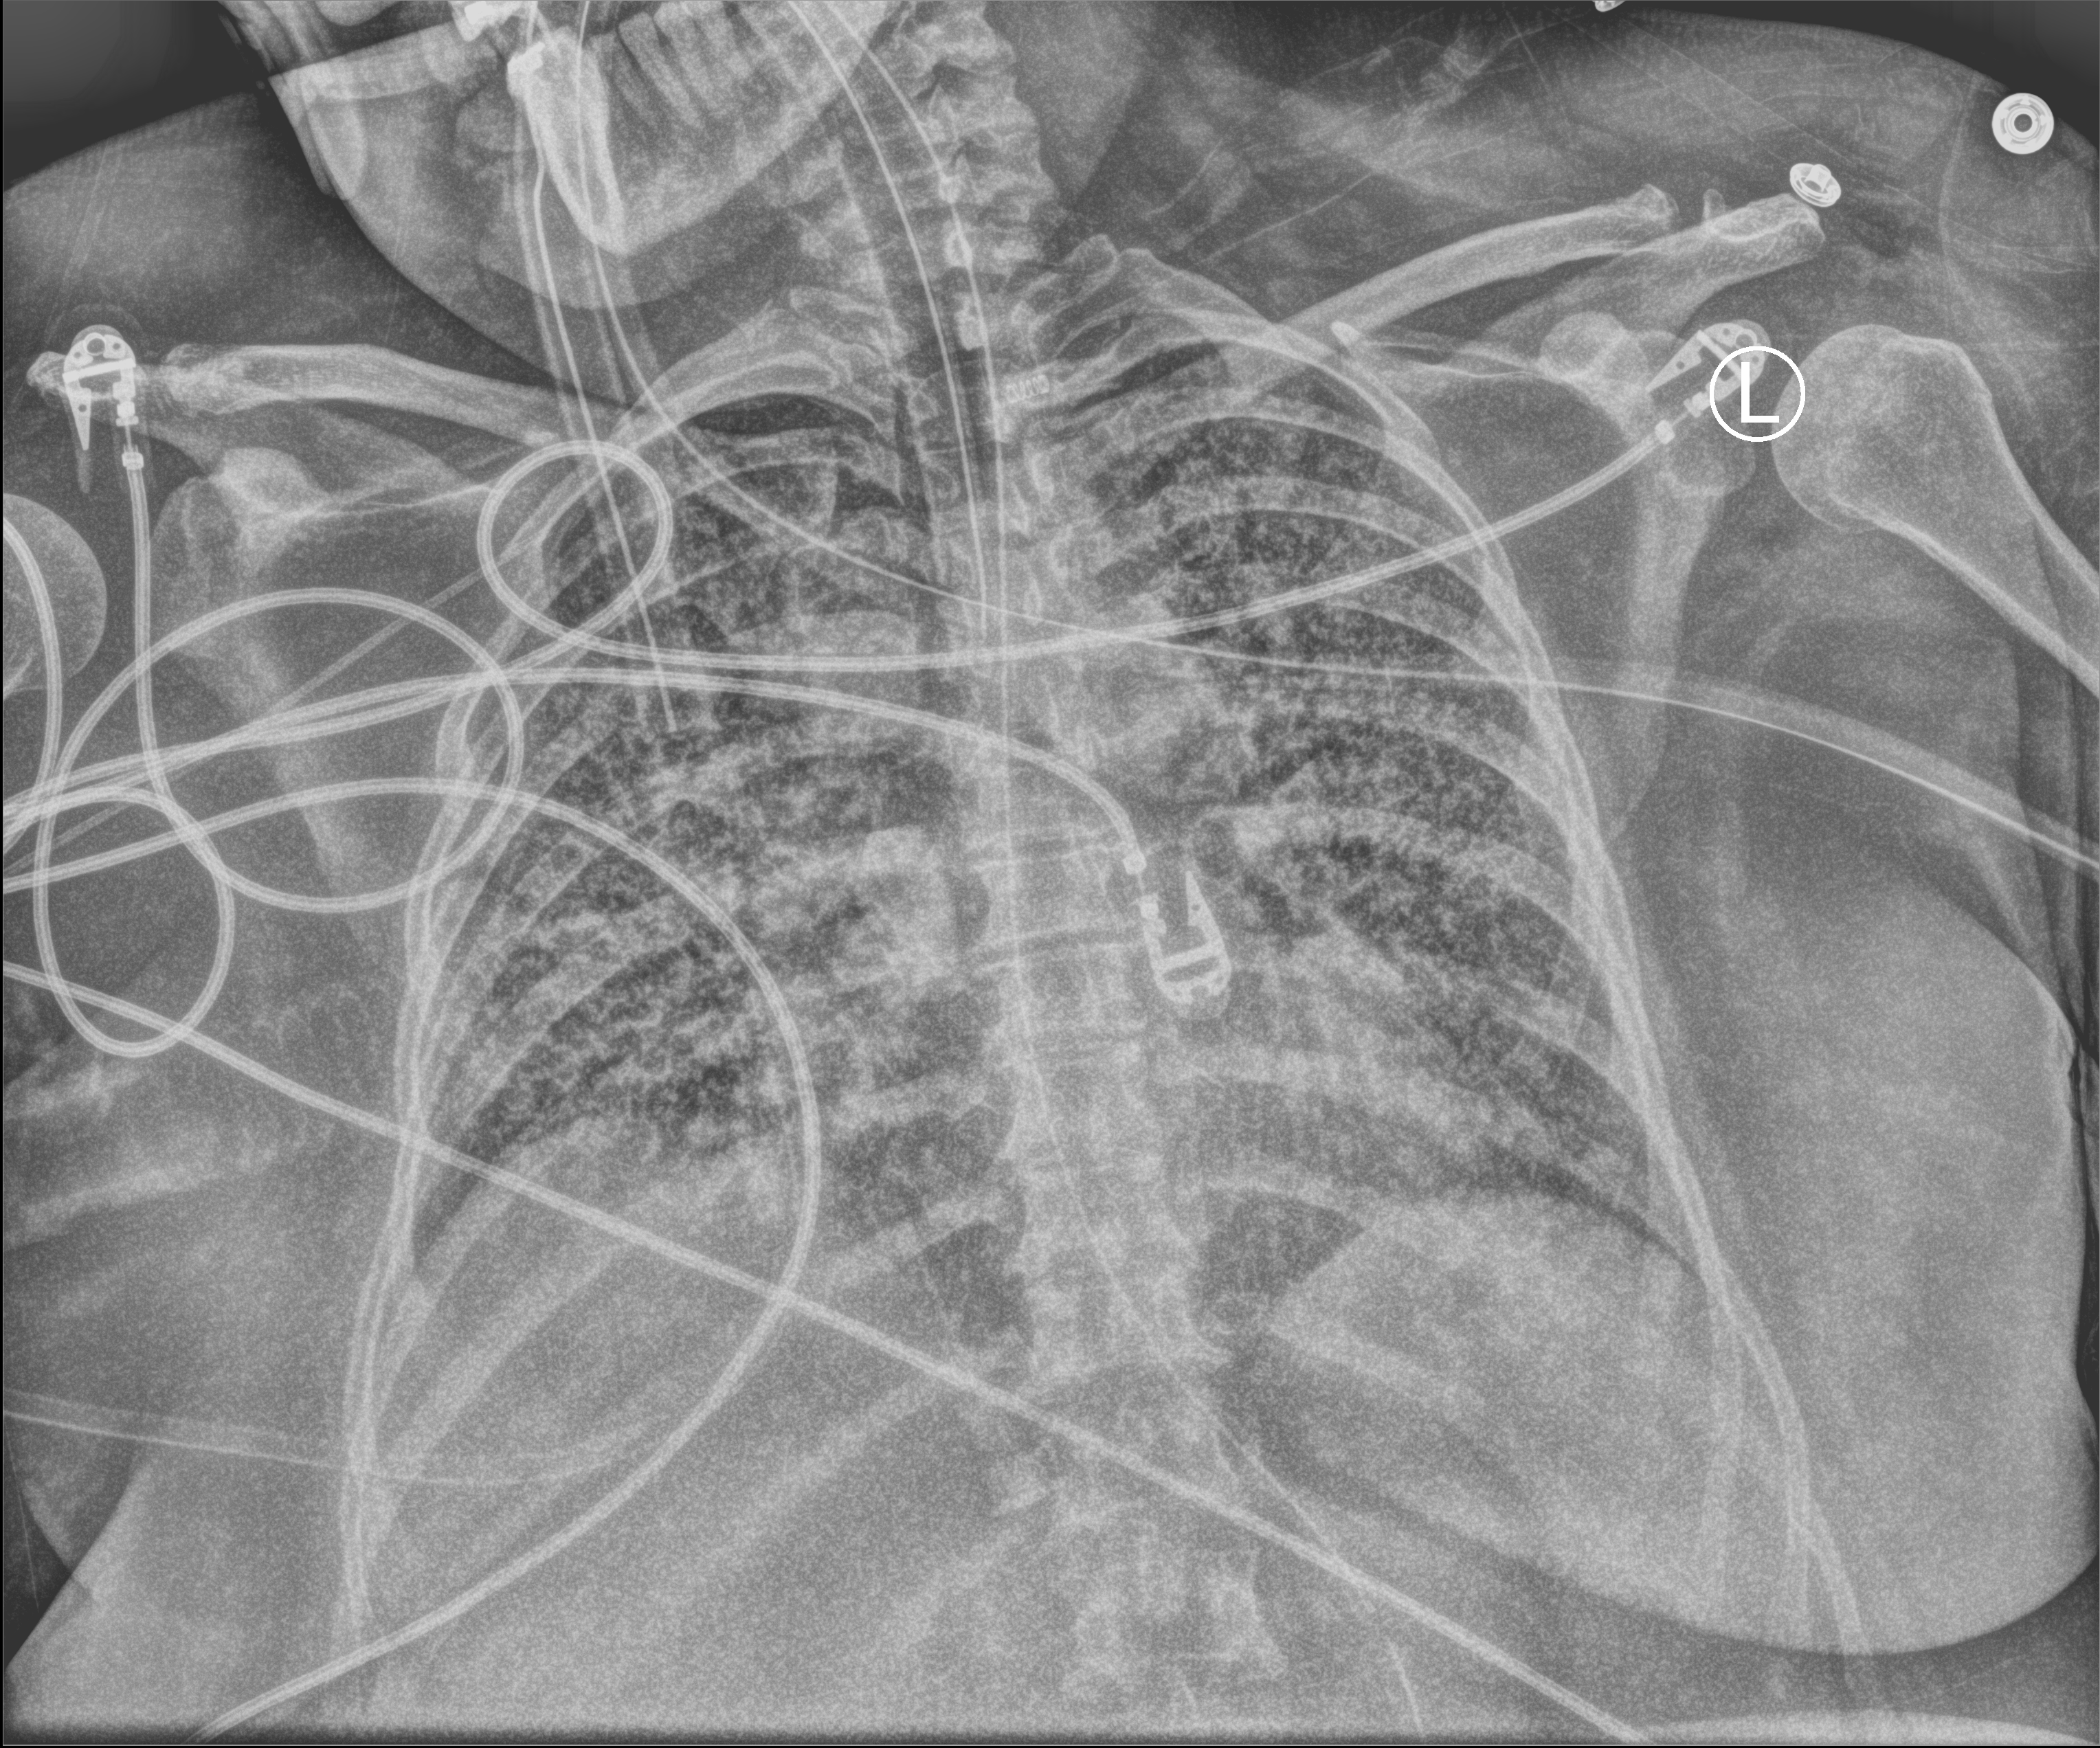
Chest X-ray (portable), anteroposterior (AP) projection. Patient hospitalised with COVID-19; female, aged 18–59 years.
Admission-level facts for this patient (not findings on this image; timing relative to this image not recorded):
- COPD (admission record): no